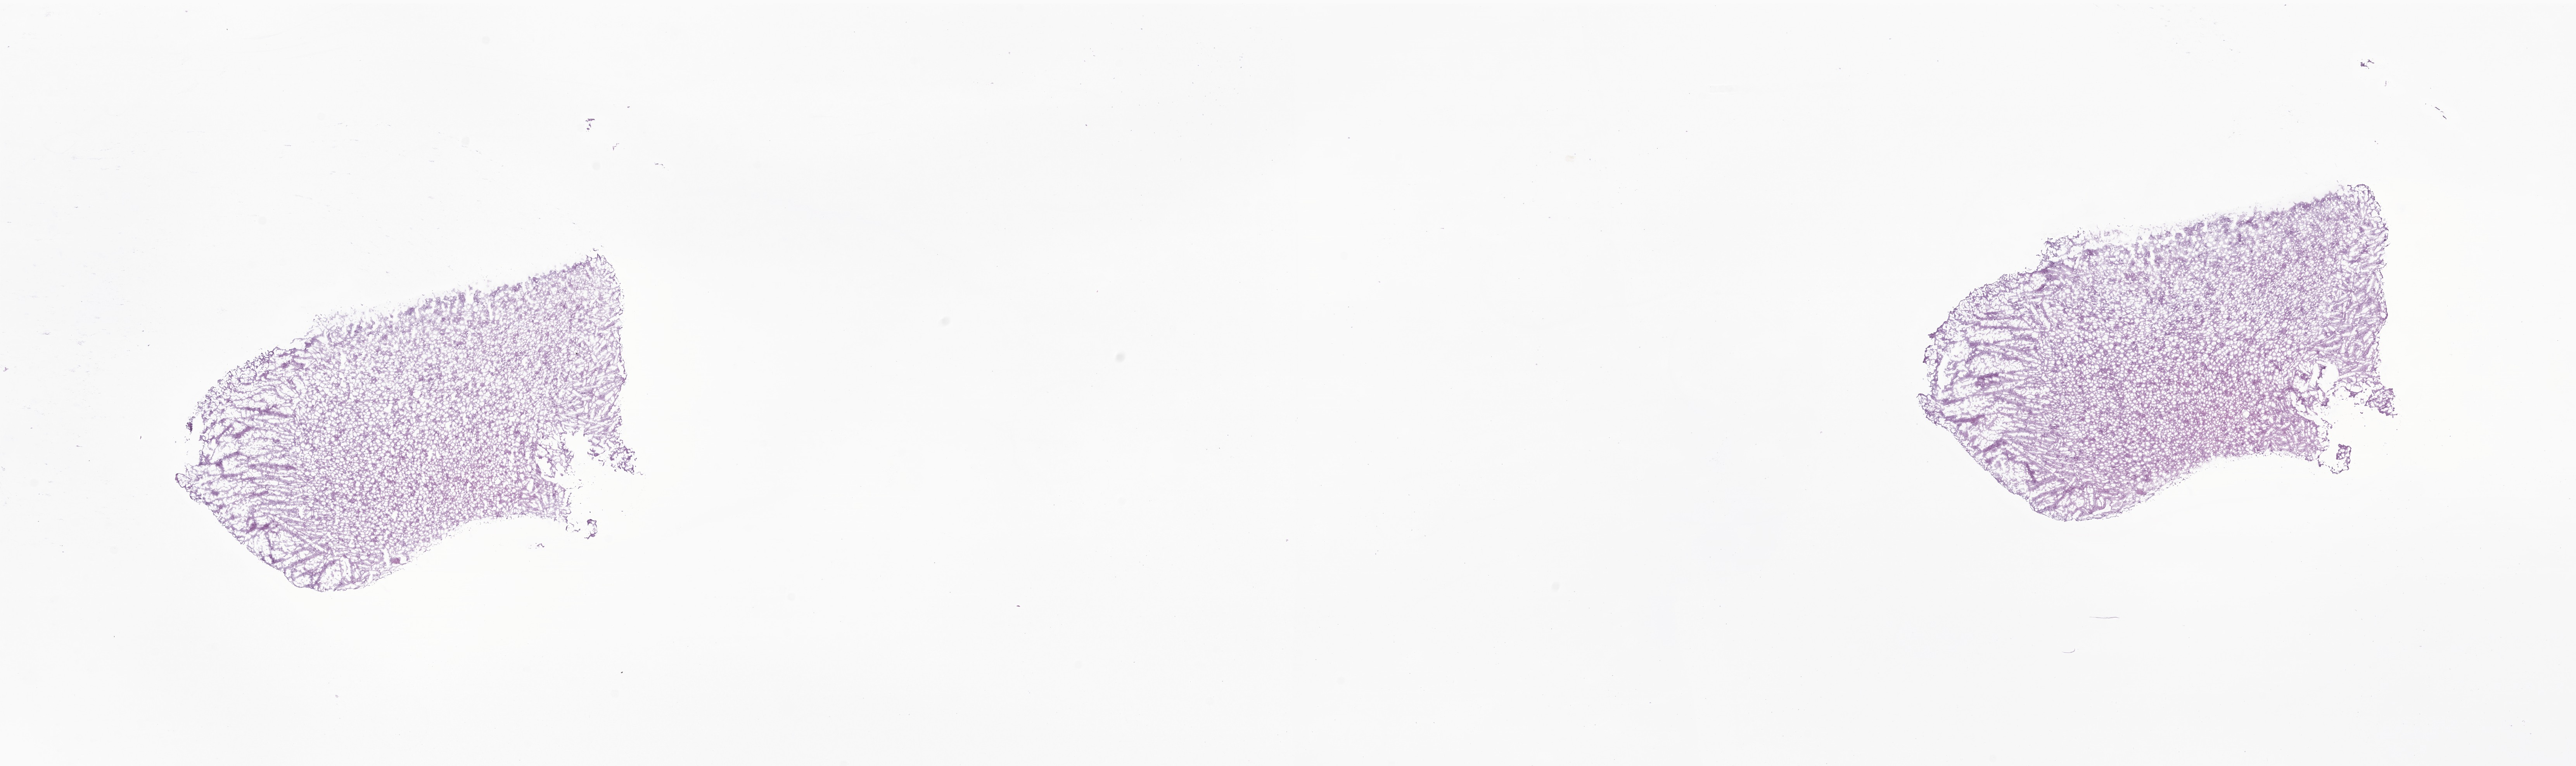
Digitized H&E-stained section of tumor tissue from the brain — a low-resolution overview of the entire scanned area, about 28.0 x 8.3 mm; cryosection (OCT / tissue freezing medium). Patient male; age 62 months (5 years 2 months).
Recorded diagnosis: Neoplasm, uncertain whether benign or malignant.